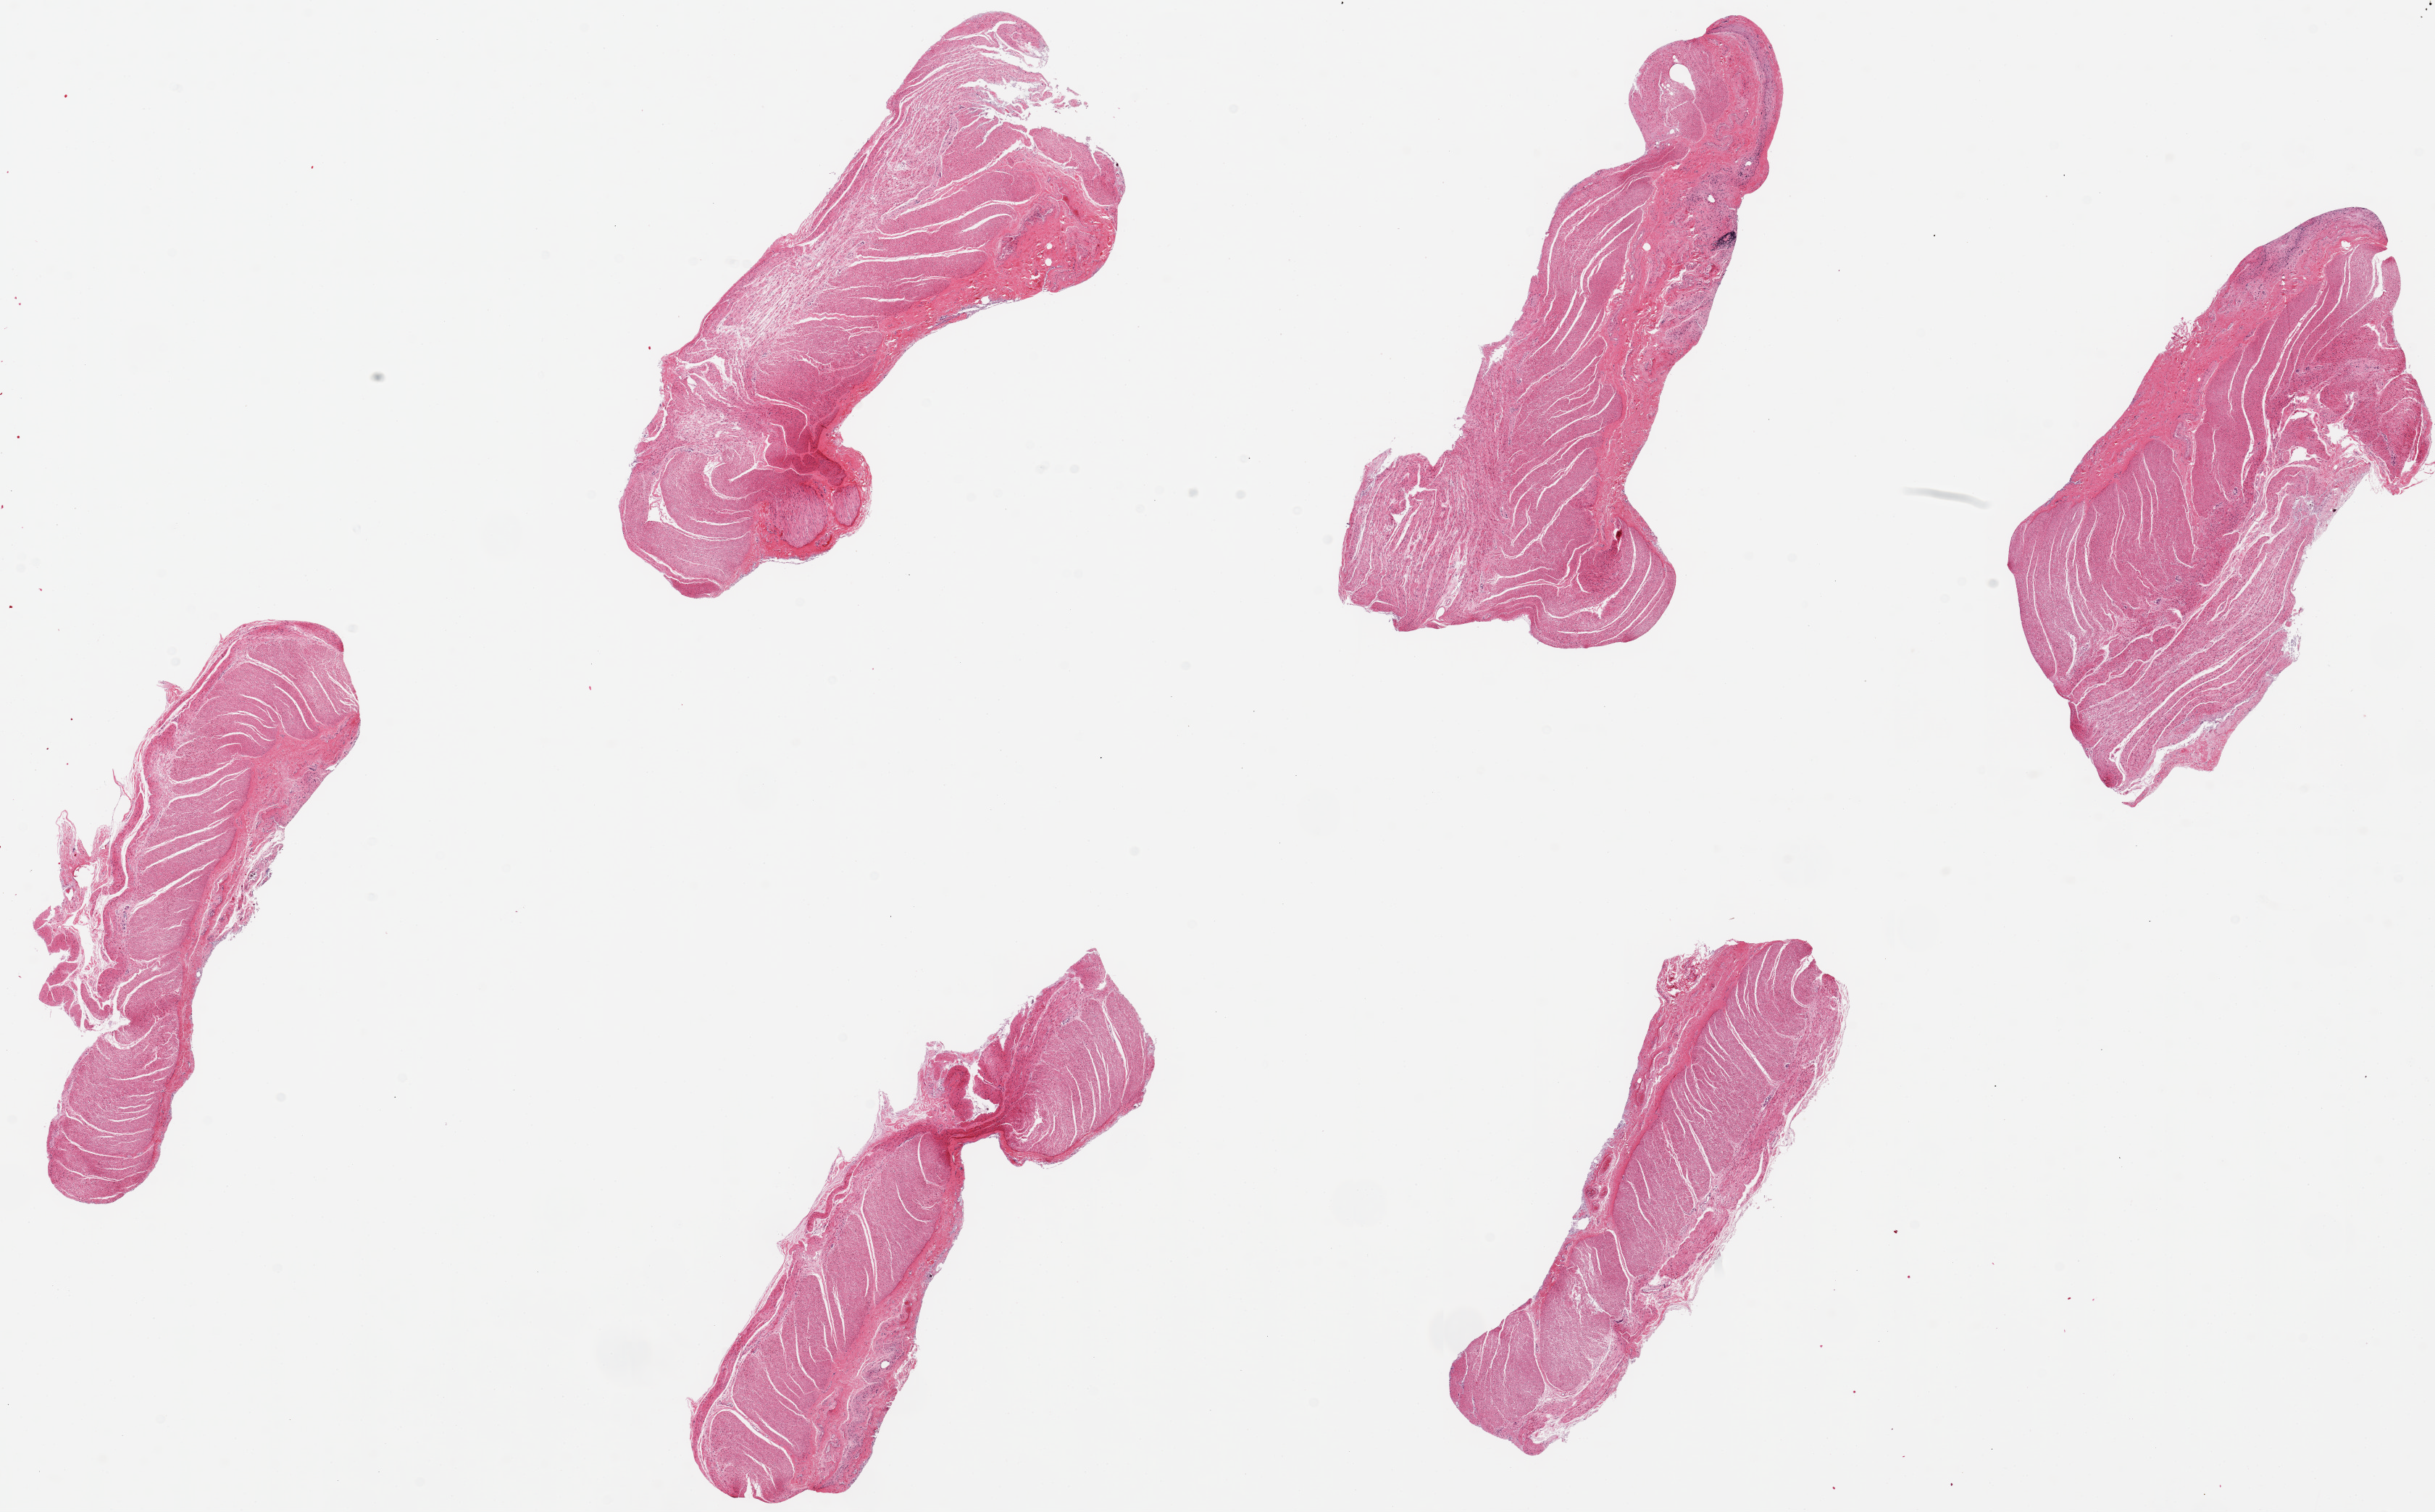
Haematoxylin and eosin whole-slide image — low-resolution overview of the scanned area, about 26.6 x 16.5 mm (from a 20x scan); PAXgene-fixed, paraffin-embedded tissue; section of sigmoid colon (target tissue); tissue donor sample. Donor: female.
- review note (as recorded): 6 pieces. up to 7.5x4mm; All muscle and some fibrous stroma (good)